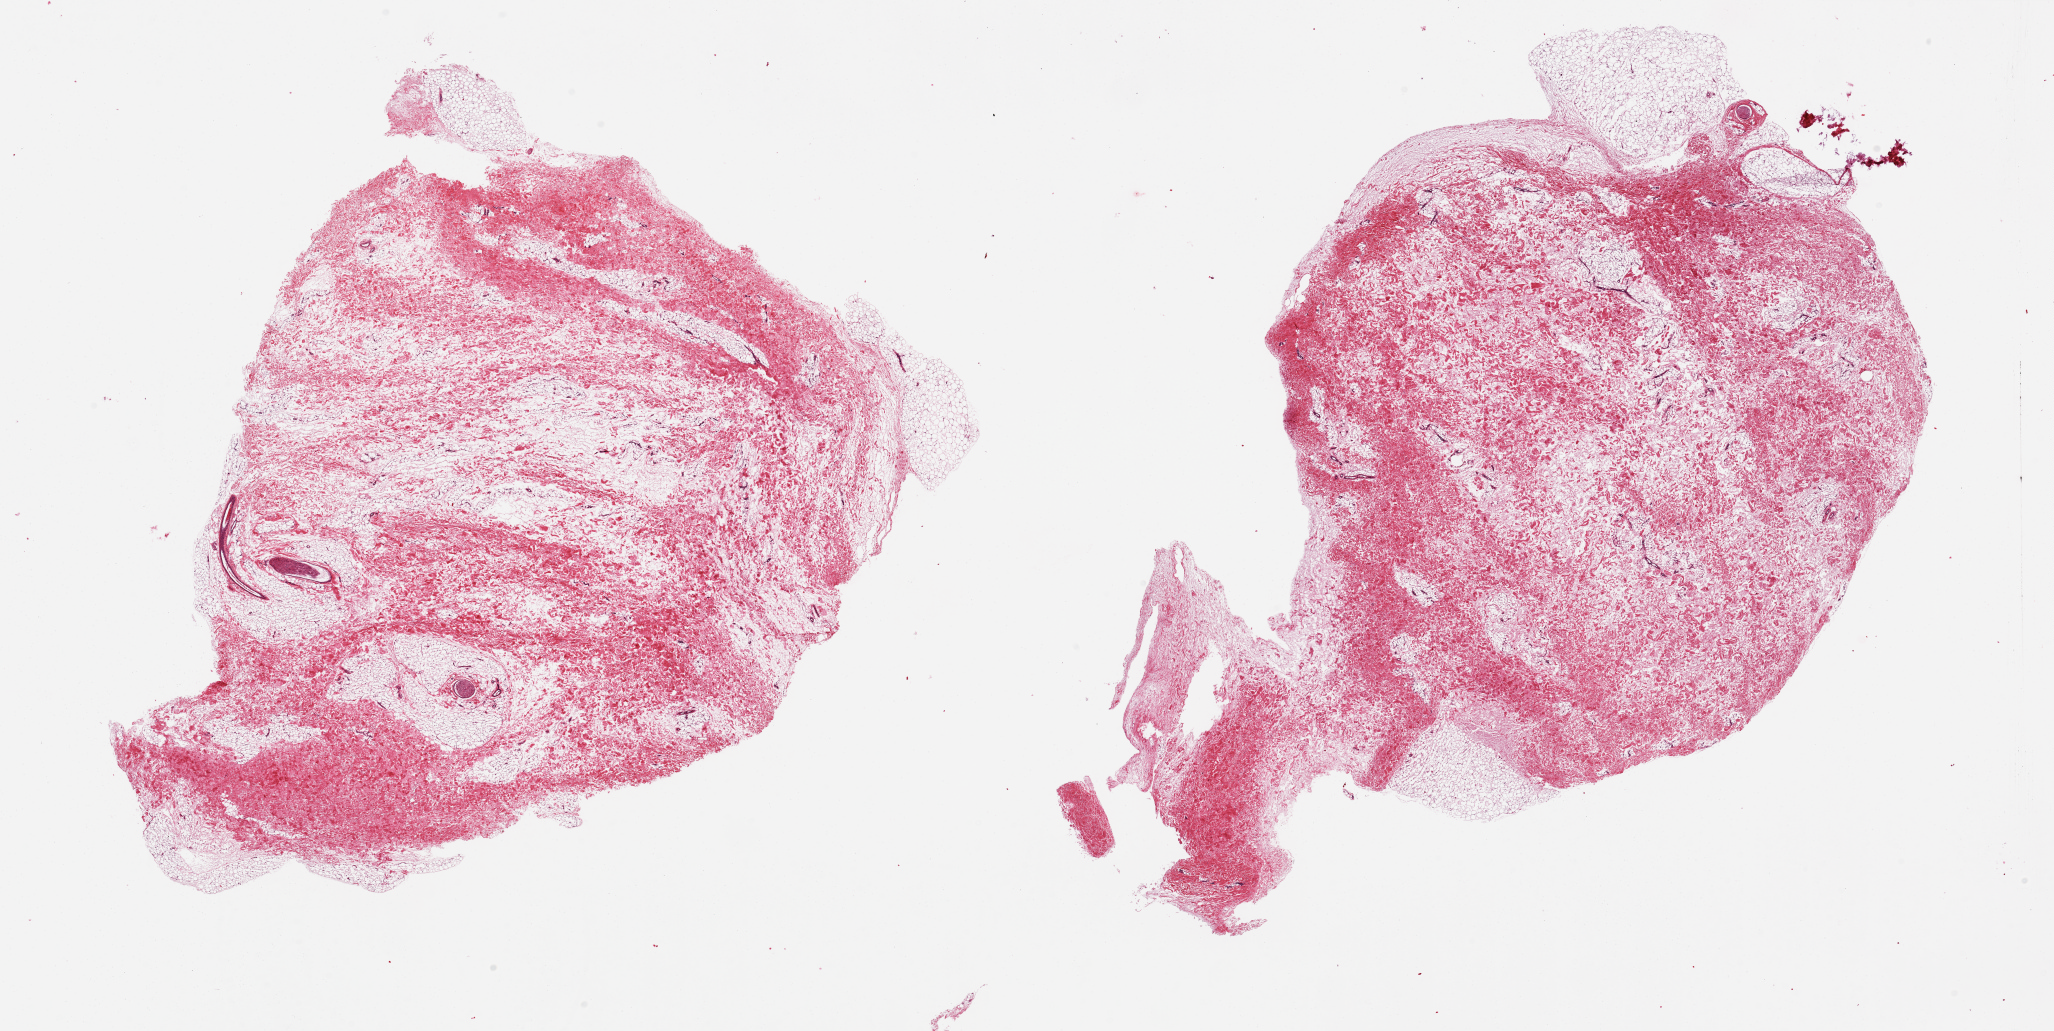
Digitized haematoxylin and eosin-stained section — low-resolution overview of the scanned area, about 32.5 x 16.3 mm, PAXgene-fixed, paraffin-embedded tissue, section of breast (target tissue), donor tissue sample. Male donor.
Review note (as recorded): 2 pieces, fibroadipose stroma; no ductal elements present.